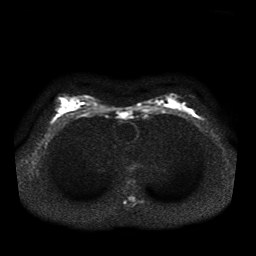
Breast MRI, one axial slice; slice 23 of 41 in the series (ordered by position); diffusion-weighted series; image 2 of 4 stored at this slice position (different b-values; order by instance number); 1.5 T; 5 mm slice thickness; 256 × 256 image matrix, field of view 330 × 330 mm. Female patient.
Outlined on this slice (manually delineated by an expert):
- tumour on diffusion-weighted imaging: bounding box (x1, y1, x2, y2) in pixels: (187, 110, 192, 113)